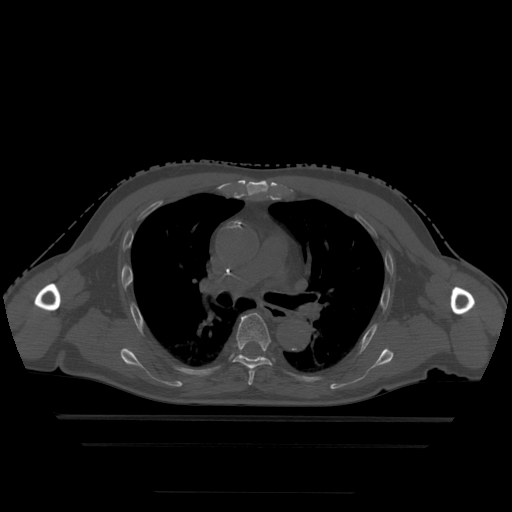
CT including the spine, one axial slice; position 319 of 522 along the scan axis; bone window (W 1800 / L 400 HU); 1.25 mm slice thickness; 512 × 512 image matrix, field of view 436 × 436 mm. Patient age 68 years. From the clinical record (not read from this slice): primary cancer: urothelial.
Annotated regions visible in this slice (semi-automatic segmentation, software-assisted and operator-edited):
- T5 vertebra: bounding box [x1, y1, x2, y2] px = [248, 370, 255, 386]
- T6 vertebra: [234, 314, 272, 370]